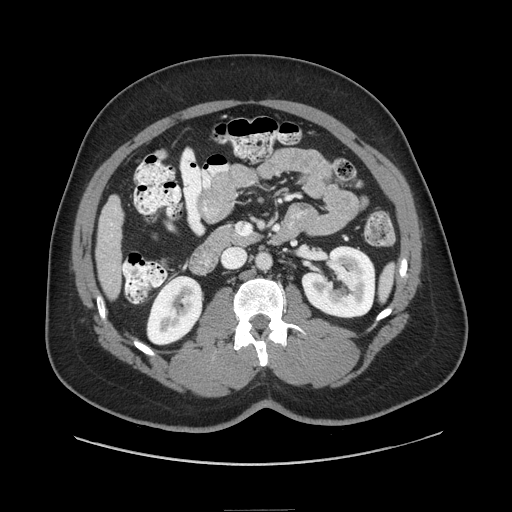
Contrast-enhanced abdominal CT (liver protocol), one axial slice; slice 20 of 87 in the series (ordered by position); 140 kVp; soft-tissue window (W 400 / L 40 HU); 2.5 mm slice thickness; 512 × 512 image matrix, field of view 440 × 440 mm. Case-level facts recorded for this patient, not image findings: diagnosis: hepatocellular carcinoma (patient treated with transarterial chemoembolisation; whether this scan precedes or follows treatment is not stated here); TNM stage (as recorded): Stage-II; Child-Pugh class: A; tumour differentiation: moderately differentiated; tumour nodularity: uninodular.
Outlined on this slice (semi-automatic segmentation, software-assisted and operator-edited):
- liver parenchyma outside the tumour (the mass and vessels are separate outlines, so this box may not span the whole liver): bounding box [x1, y1, x2, y2] px = [96, 196, 122, 298]
- liver vessels: [110, 223, 113, 225]